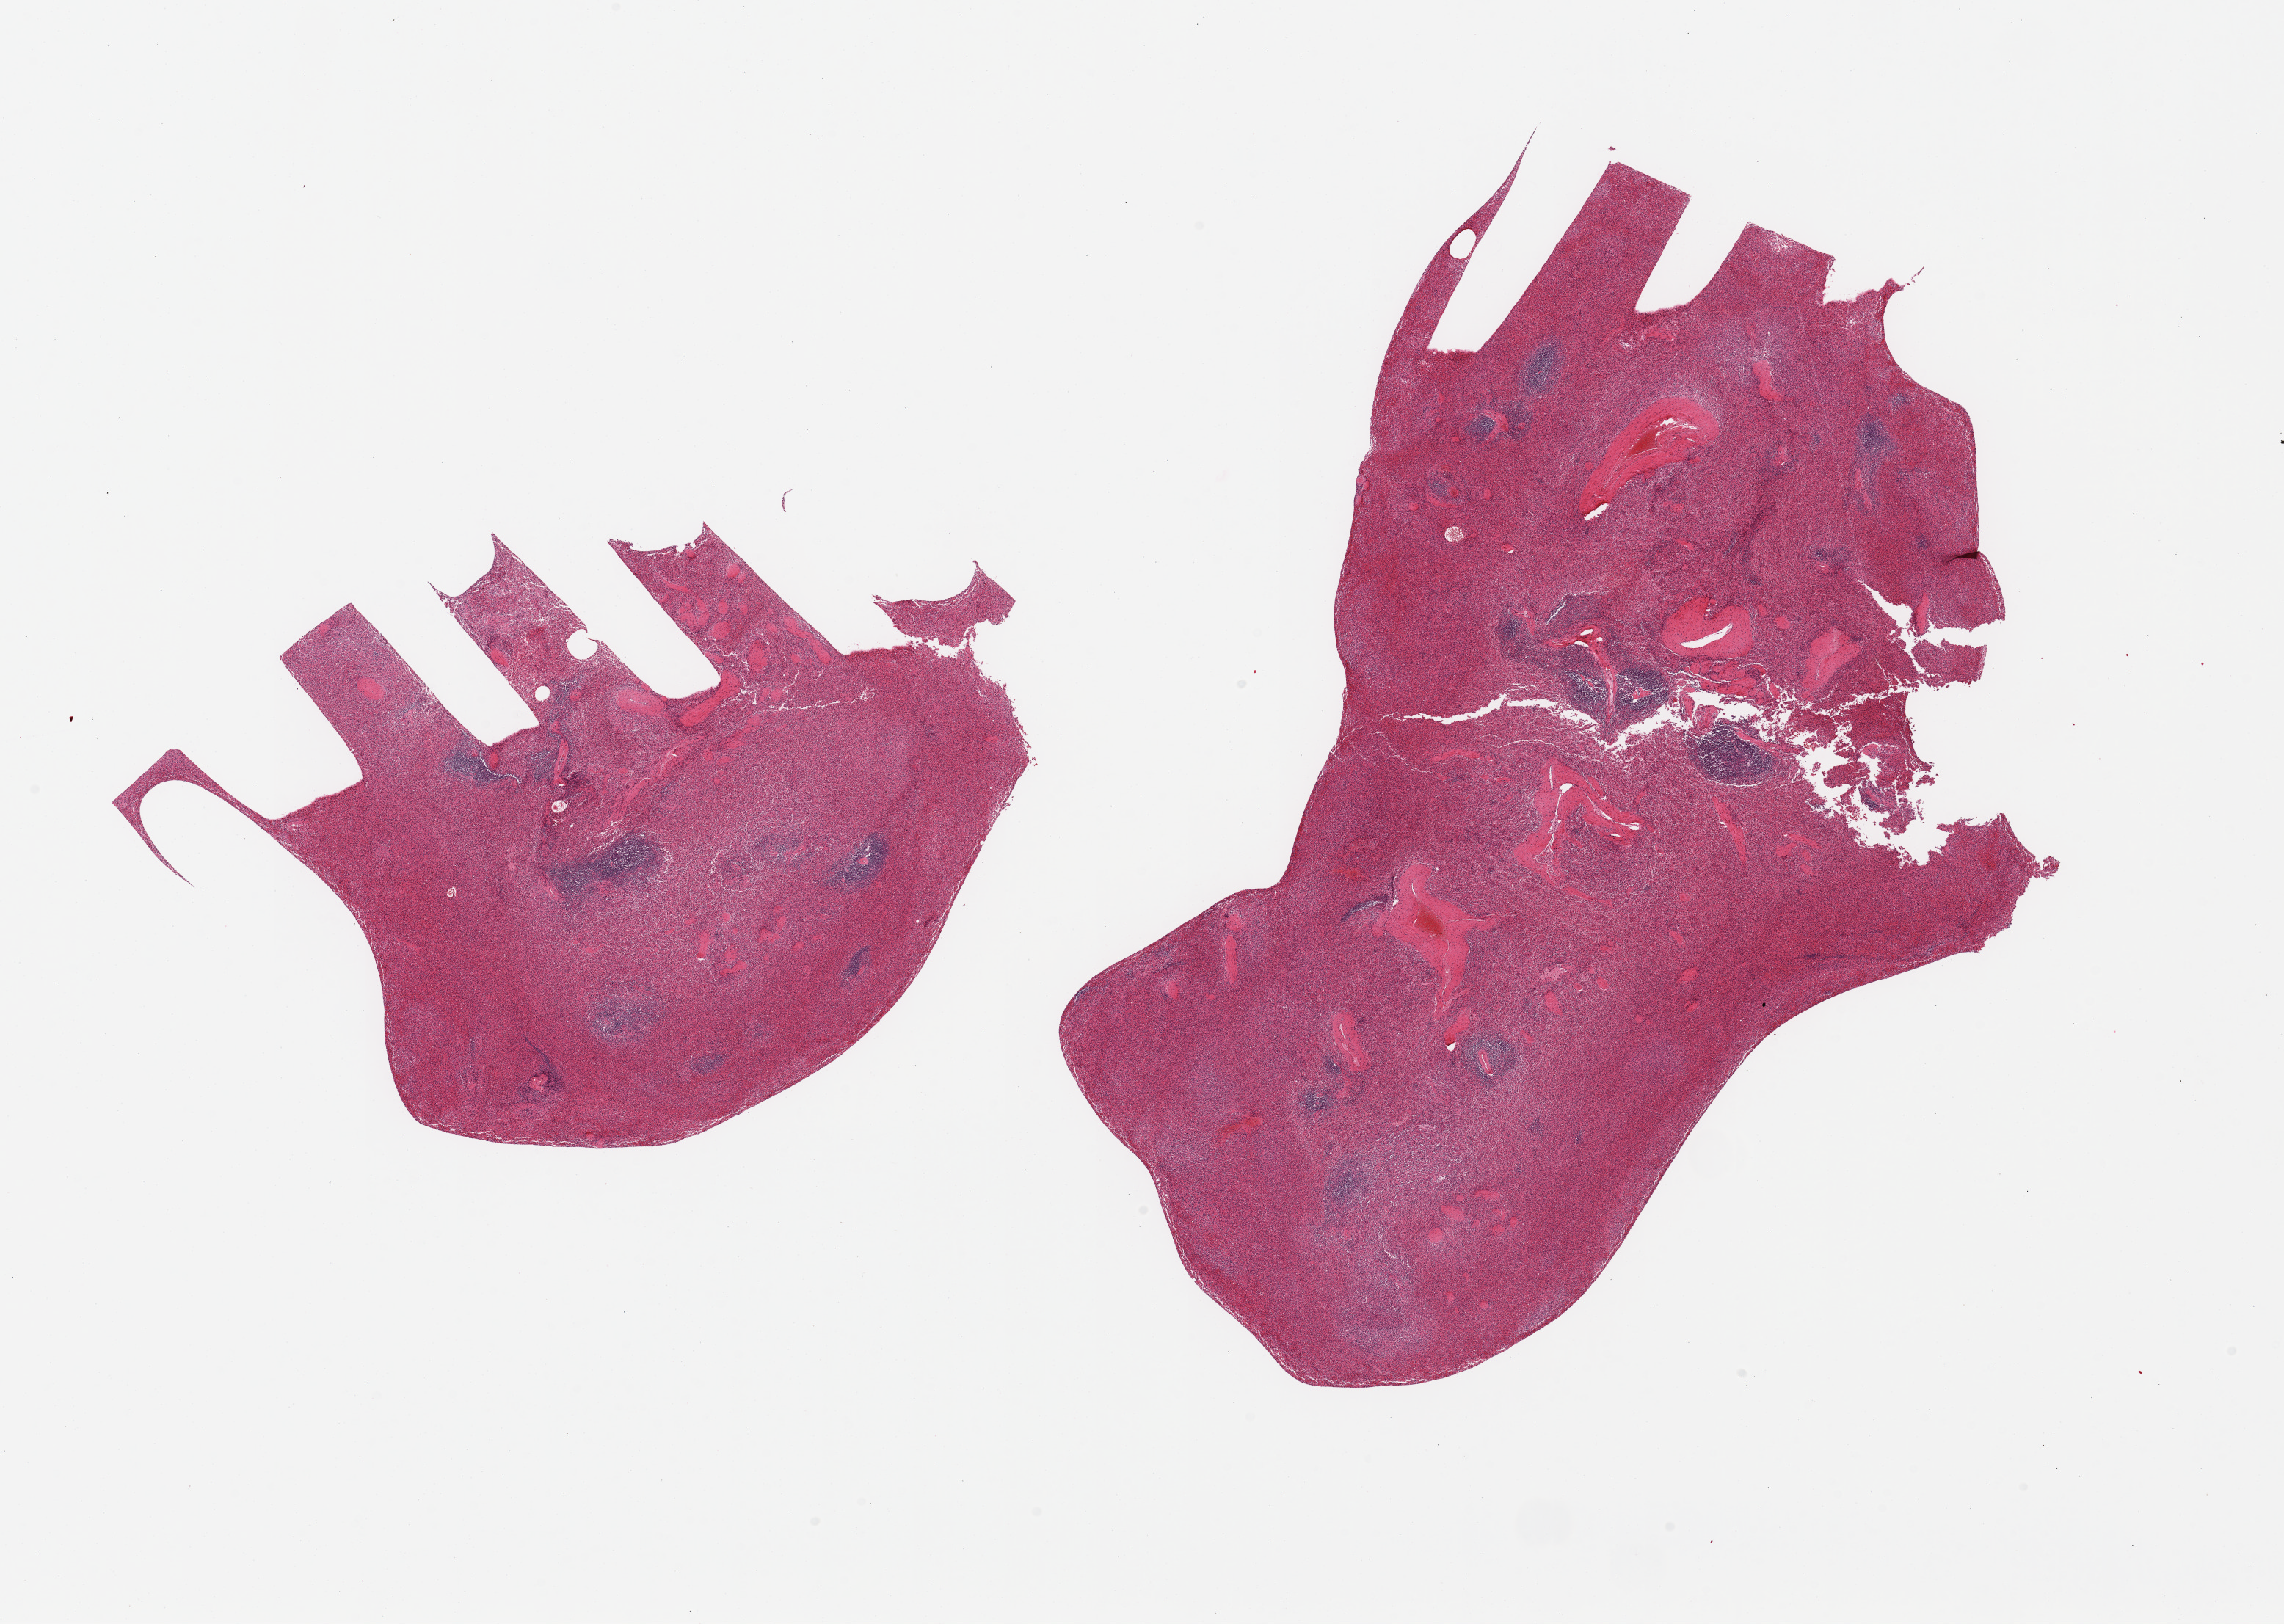
Digitized haematoxylin and eosin-stained section — low-resolution overview of the scanned area, about 24.6 x 17.5 mm, PAXgene-fixed, paraffin-embedded tissue, sampled site (target tissue): spleen, donor tissue sample. Female donor.
Pathologist's review note for this sample: 2 pieces; slightly congested.